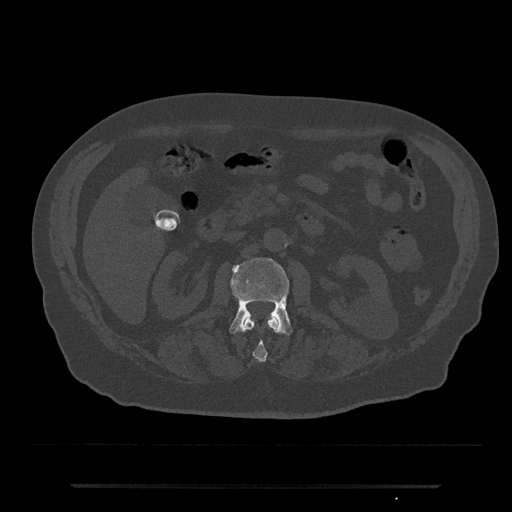
CT including the spine, one axial slice. Position 494 of 797 along the scan axis. Reconstruction kernel Br40s/3. 120 kVp. Bone window (W 1800 / L 400 HU). 0.5 mm slice thickness. 512 × 512 image matrix, field of view 434 × 434 mm. Patient: male, 80 years. From the clinical record (not read from this slice): primary cancer: prostate; vertebrae with lytic lesions (as recorded): L1, T11.
Annotated regions visible in this slice (semi-automatic segmentation, software-assisted and operator-edited):
- L1 vertebra: bounding box <242,316,281,362> (left, top, right, bottom; pixels)
- L2 vertebra: <229,258,293,335>